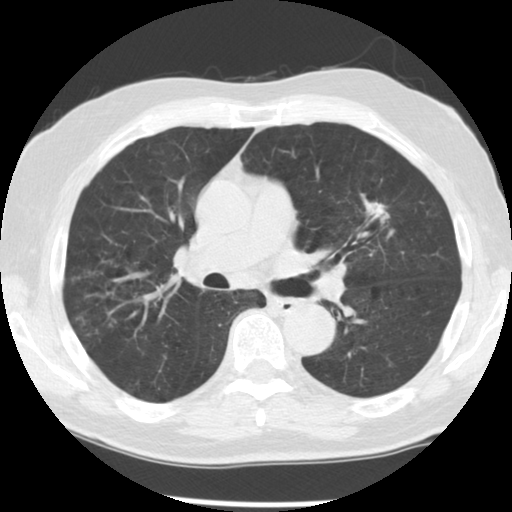
Low-dose screening chest CT, axial slice. Third screening round (two years after baseline). Lung window (W 1500 / L -600 HU). 2.5 mm slice thickness. Standard (soft-tissue) reconstruction kernel (STANDARD). 140 kVp. Slice 75 of 131 in the series. Male, age 70 years at enrolment. Current smoker at enrolment.
• Expert reader's lesion annotation, bounding box <356,185,410,241> (left, top, right, bottom; pixels).
• The screening reader recorded 3 non-calcified nodules or masses ≥4 mm on this exam; which of them this box marks is not recorded.
• Official screen result: positive, other.
• Lung cancer was diagnosed 74 days after this screen: adenocarcinoma, NOS, left upper lobe, moderately differentiated (G2), stage IIIA (AJCC 6th edition), 17 mm at pathology.